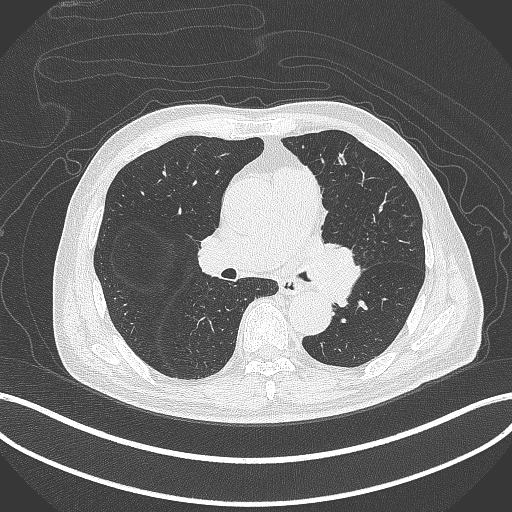
Chest CT, one axial slice; slice 240 of 417 in the series (ordered by position); reconstruction kernel B70f; 120 kVp; lung window (W 1500 / L -600 HU); 512 × 512 image matrix. Patient: male, 77 years. Case-level facts recorded for this patient, not image findings: clinical TNM (as recorded): T3 N1 M0.
Outlined on this slice (bounding box drawn by a radiologist):
- lung tumour (recorded histology: adenocarcinoma): bounding box [x1, y1, x2, y2] px = [306, 237, 364, 309]